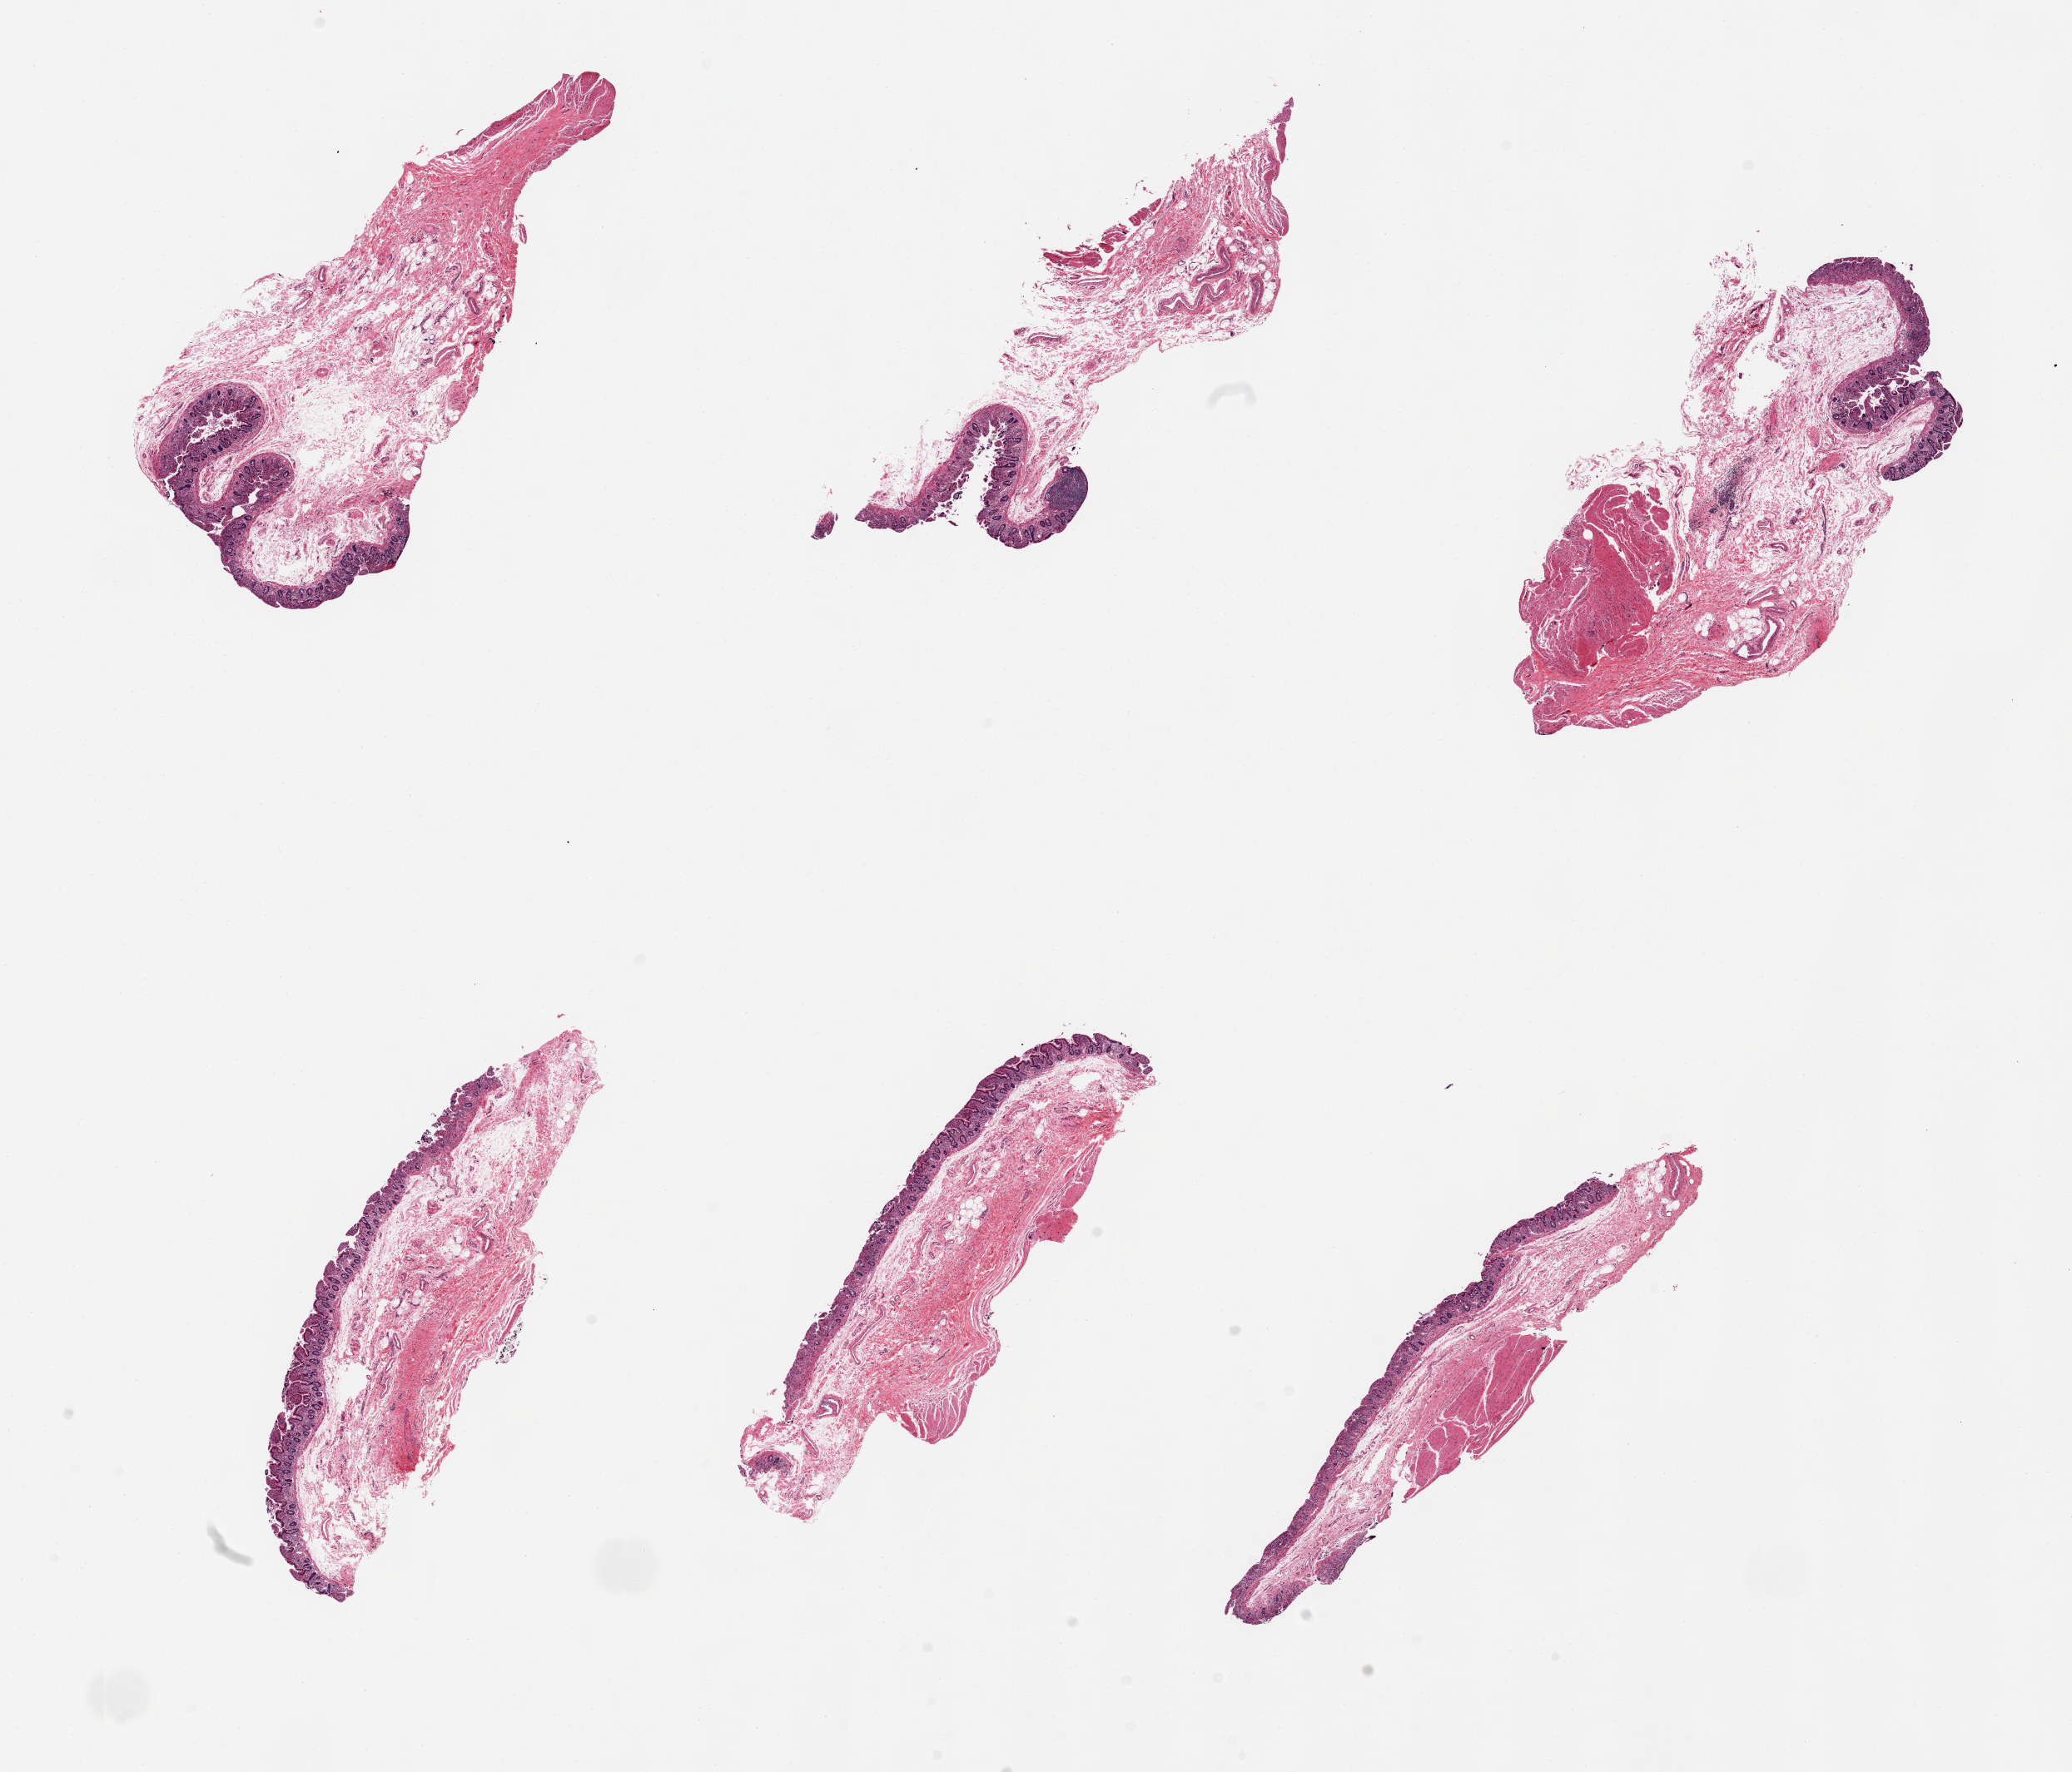
H&E whole-slide image, shown as a low-resolution overview of the whole scanned area (about 19.7 x 16.8 mm); PAXgene-fixed, paraffin-embedded tissue; sampled site (target tissue): ileum; tissue donor sample. Donor: male.
Review note (as recorded): 6 pieces; only one lymphoid aggregate 0.4 mm.